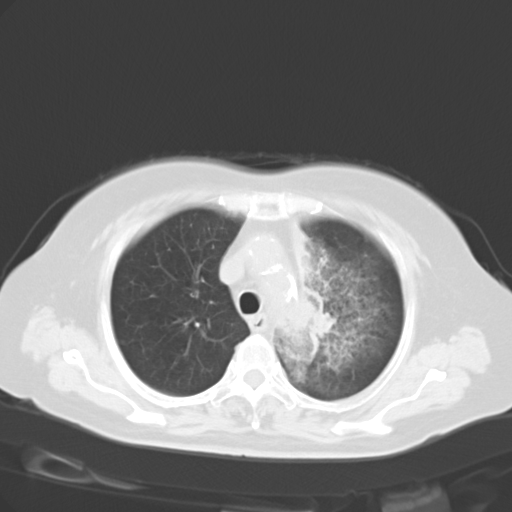
Chest CT, one axial slice. Slice 21 of 27 in the series (ordered by position). 120 kVp. Lung window (W 1500 / L -600 HU). 10 mm slice thickness. 512 × 512 image matrix, field of view 353 × 353 mm. Patient: female, 65 years. From the clinical record (not read from this slice): clinical TNM (as recorded): T2b N1 M0.
Outlined on this slice (bounding box drawn by a radiologist):
- lung tumour (recorded histology: adenocarcinoma): bounding box <302,290,337,358> (left, top, right, bottom; pixels)